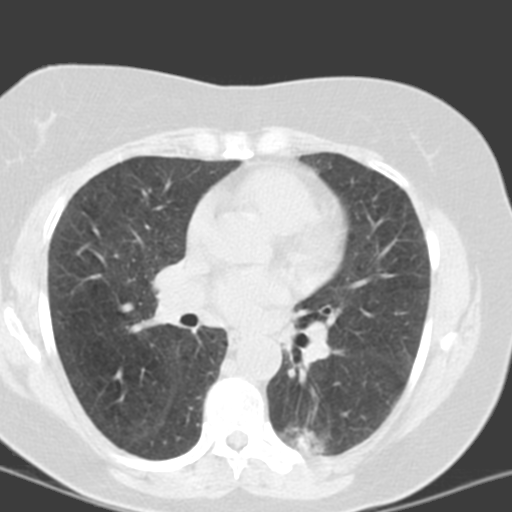
Low-dose screening chest CT, axial slice. Third screening round (two years after baseline). Lung window (W 1500 / L -600 HU). 3.2 mm slice thickness. 120 kVp. Female, age 55 years at enrolment. Current smoker at enrolment.
Expert reader's lesion annotation, box from (x=283, y=409) to (x=362, y=463) px. The screening reader recorded 6 non-calcified nodules or masses ≥4 mm on this exam (left lower lobe, left lower lobe, left upper lobe, lingula, lingula, right middle lobe); which of them this box marks is not recorded. Lung cancer was diagnosed 357 days after this screen: adenocarcinoma with mixed subtypes, left lower lobe, poorly differentiated (G3), stage IA (AJCC 6th edition), 21 mm at pathology.